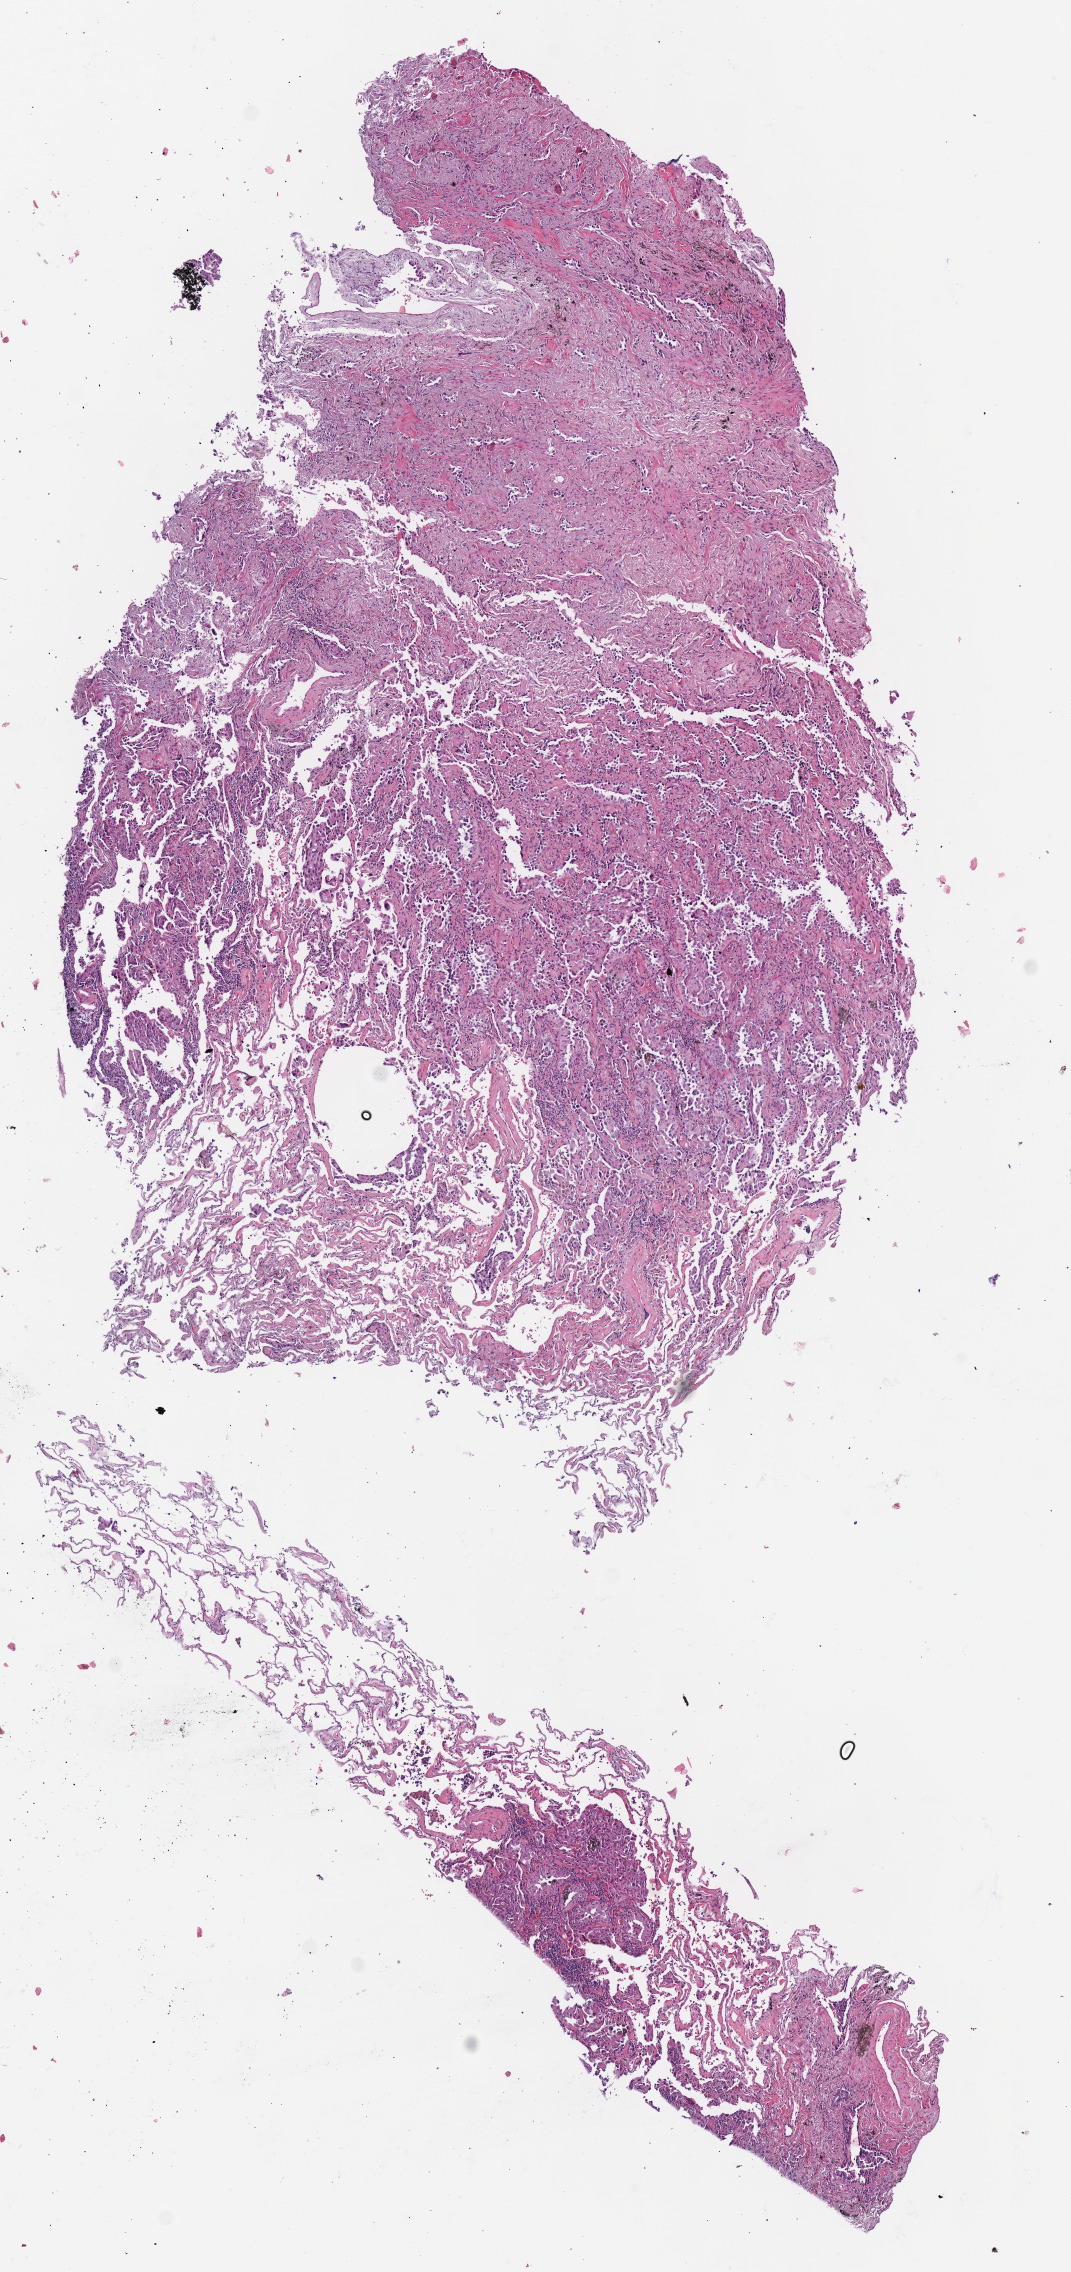
Whole-slide histology image, H&E-stained, shown as a low-resolution overview of the whole scanned area (about 4.2 x 8.9 mm); frozen section from the top of the tissue portion; primary tumour sample from the lung. Patient: female, age at initial diagnosis 74 years. Composition of this section per pathologist review: tumour cells 52%, tumour nuclei 60%, normal cells 18%, stromal cells 30%, necrosis 0%.
Histologic diagnosis: Bronchiolo-alveolar carcinoma, non-mucinous (lower lobe, lung). Laterality: right. TNM: T4 N0 M0. AJCC pathologic stage: IIIA.